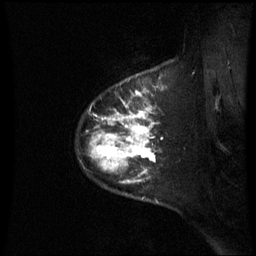
Breast MRI (dynamic contrast-enhanced), one sagittal slice. Position 51 of 60 along the scan axis. Dynamic contrast-enhanced series, image 2 of 3 at this slice position (ordered by acquisition). 1.5 T. TE 4.2 ms, TR 8.9 ms. 2.4 mm slice thickness. 256 × 256 image matrix, field of view 210 × 210 mm. Patient: female, 42 years. Case-level facts recorded for this patient, not image findings: setting: breast cancer imaged before/during neoadjuvant chemotherapy; receptor status: HER2-positive.
Structures marked on this image (semi-automatic segmentation, software-assisted and operator-edited):
- analysis volume of interest (the breast-tissue region the enhancement analysis was run in; not a lesion): bounding box <88,93,164,203> (left, top, right, bottom; pixels)
- tumour enhancement mask (voxels above the 70 % enhancement threshold inside the analysis volume of interest): <92,93,156,184>